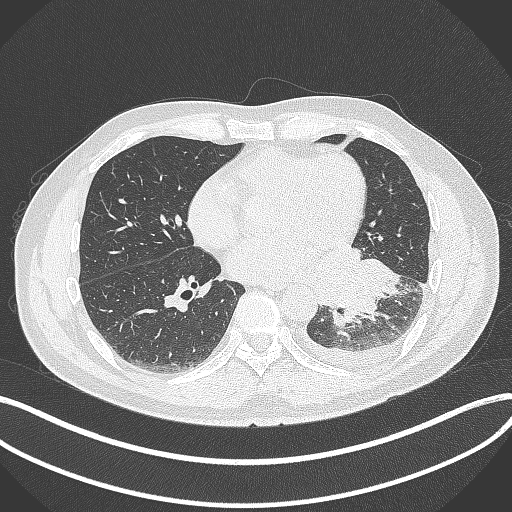
Chest CT, one axial slice; position 150 of 342 along the scan axis; reconstruction kernel B70f; 120 kVp; lung window (W 1500 / L -600 HU); 1 mm slice thickness; 512 × 512 image matrix. Male patient, age 58 years. From the clinical record (not read from this slice): clinical TNM (as recorded): T3 N1 M1b.
Outlined on this slice (bounding box drawn by a radiologist):
- lung tumour (recorded histology: small cell carcinoma): bounding box (x1, y1, x2, y2) in pixels: (311, 246, 401, 326)